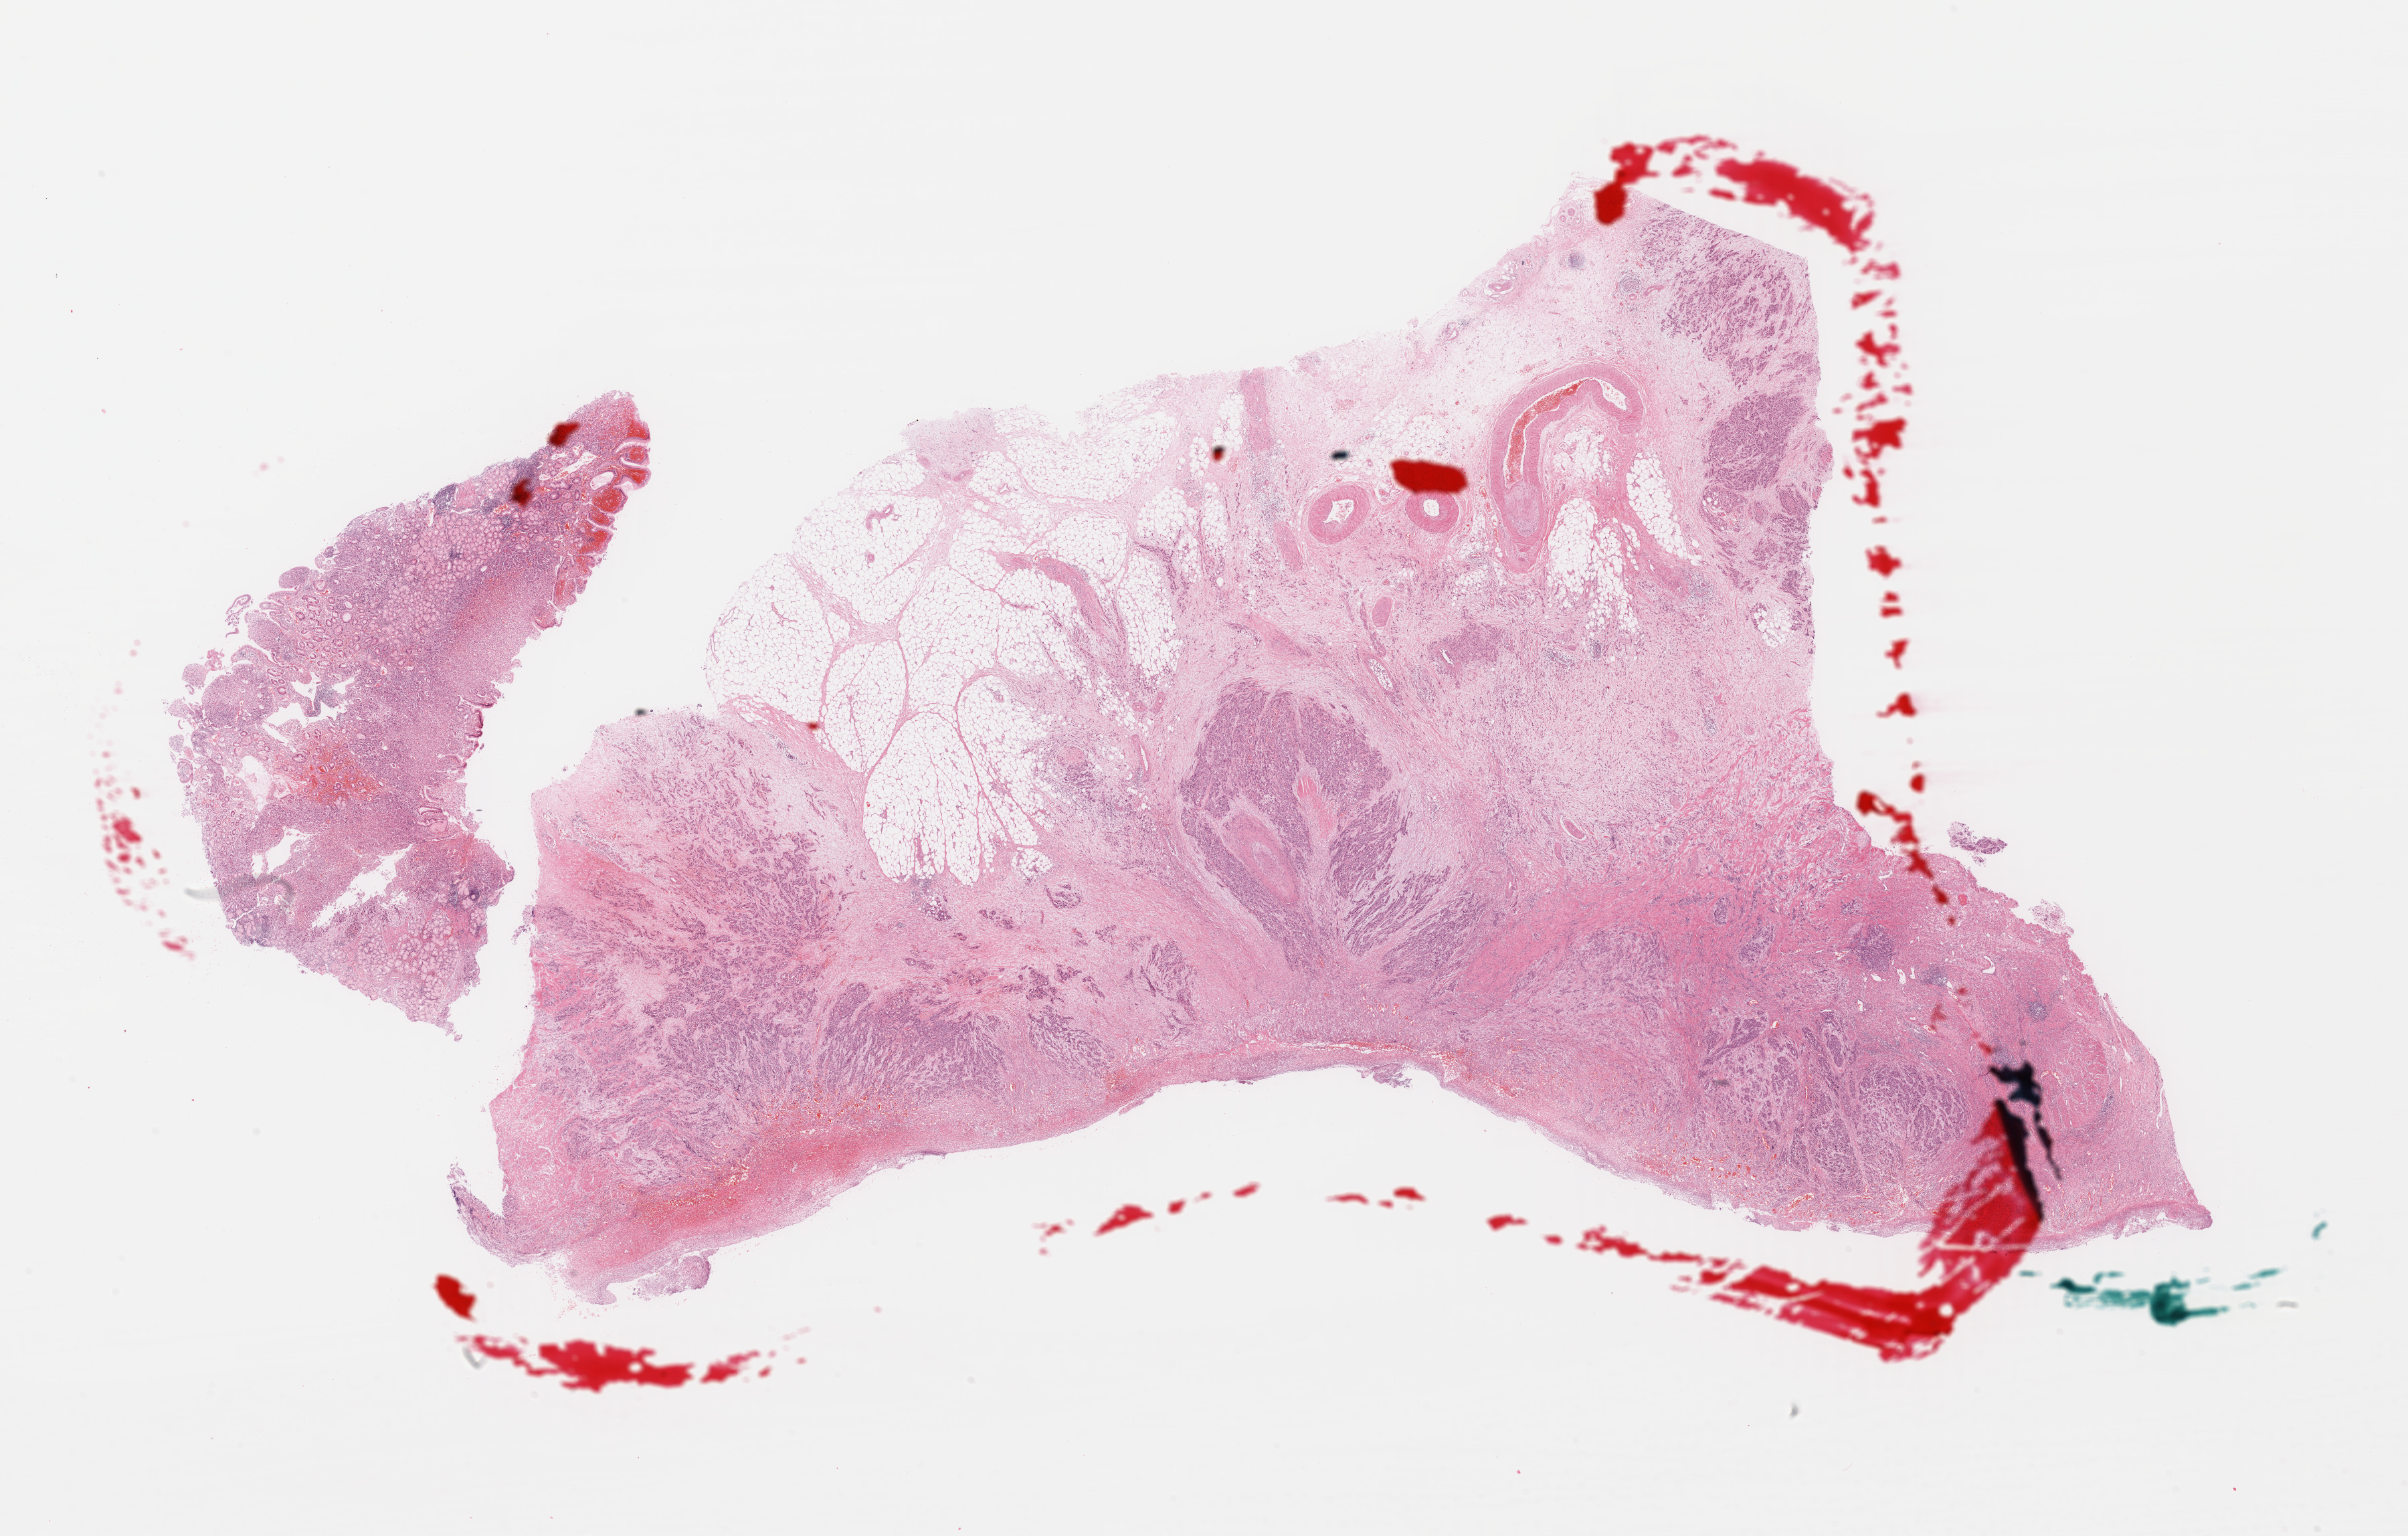
Whole-slide histology image, H&E — whole scanned area (about 28.3 x 18.0 mm) shown as a low-resolution overview, formalin-fixed paraffin-embedded (FFPE) diagnostic section, stomach, primary tumour sample. Male, age 70 years at initial diagnosis. Histologic grade: G3 (poorly differentiated).
* histologic diagnosis: Adenocarcinoma, NOS (gastric antrum)
* TNM: T3 N3a M0
* AJCC pathologic stage: IIIB